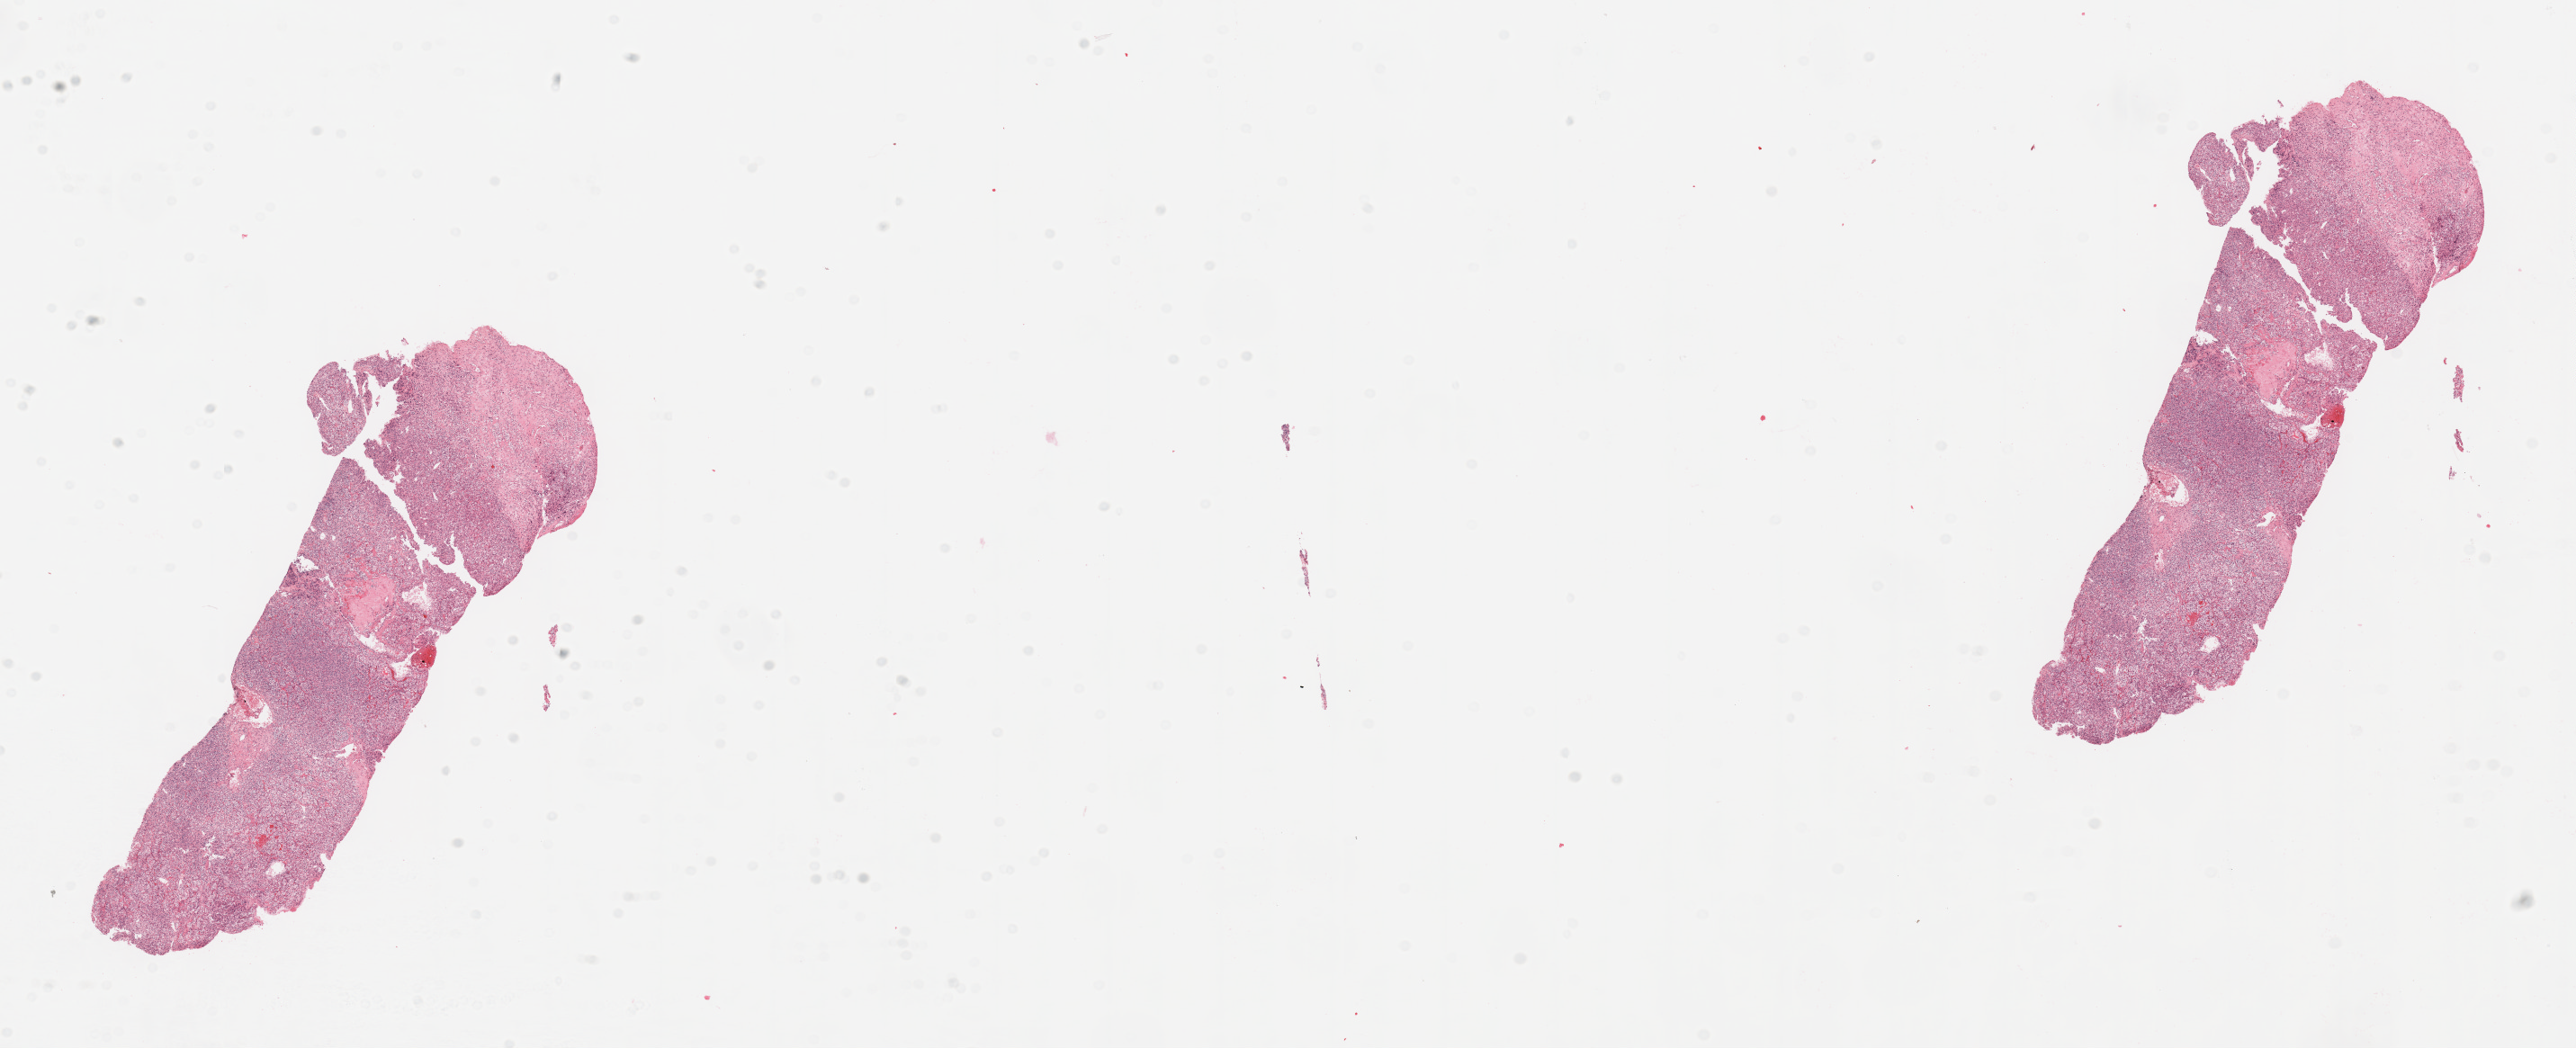
Digitized H&E-stained tissue section (whole slide) — low-resolution overview of the scanned area, about 22.6 x 9.2 mm; tumour tissue sample, sampled site: kidney. 46-year-old male patient. Composition of this section per pathologist review: tumour nuclei 90%, necrosis 5%.
Histologic diagnosis: Renal cell carcinoma, NOS.